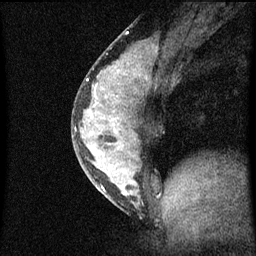
Breast MRI (dynamic contrast-enhanced), one sagittal slice. Slice 28 of 60 in the series (ordered by position). Dynamic contrast-enhanced series, image 2 of 3 at this slice position (ordered by acquisition). 1.5 T. TE 4.2 ms, TR 8 ms. 256 × 256 image matrix, field of view 180 × 180 mm. Female patient, age 33 years.
Outlined on this slice (semi-automatic segmentation, software-assisted and operator-edited):
- analysis volume of interest (the breast-tissue region the enhancement analysis was run in; not a lesion): bounding box <72,56,157,213> (left, top, right, bottom; pixels)
- tumour enhancement mask (voxels above the 70 % enhancement threshold inside the analysis volume of interest): <76,62,148,195>